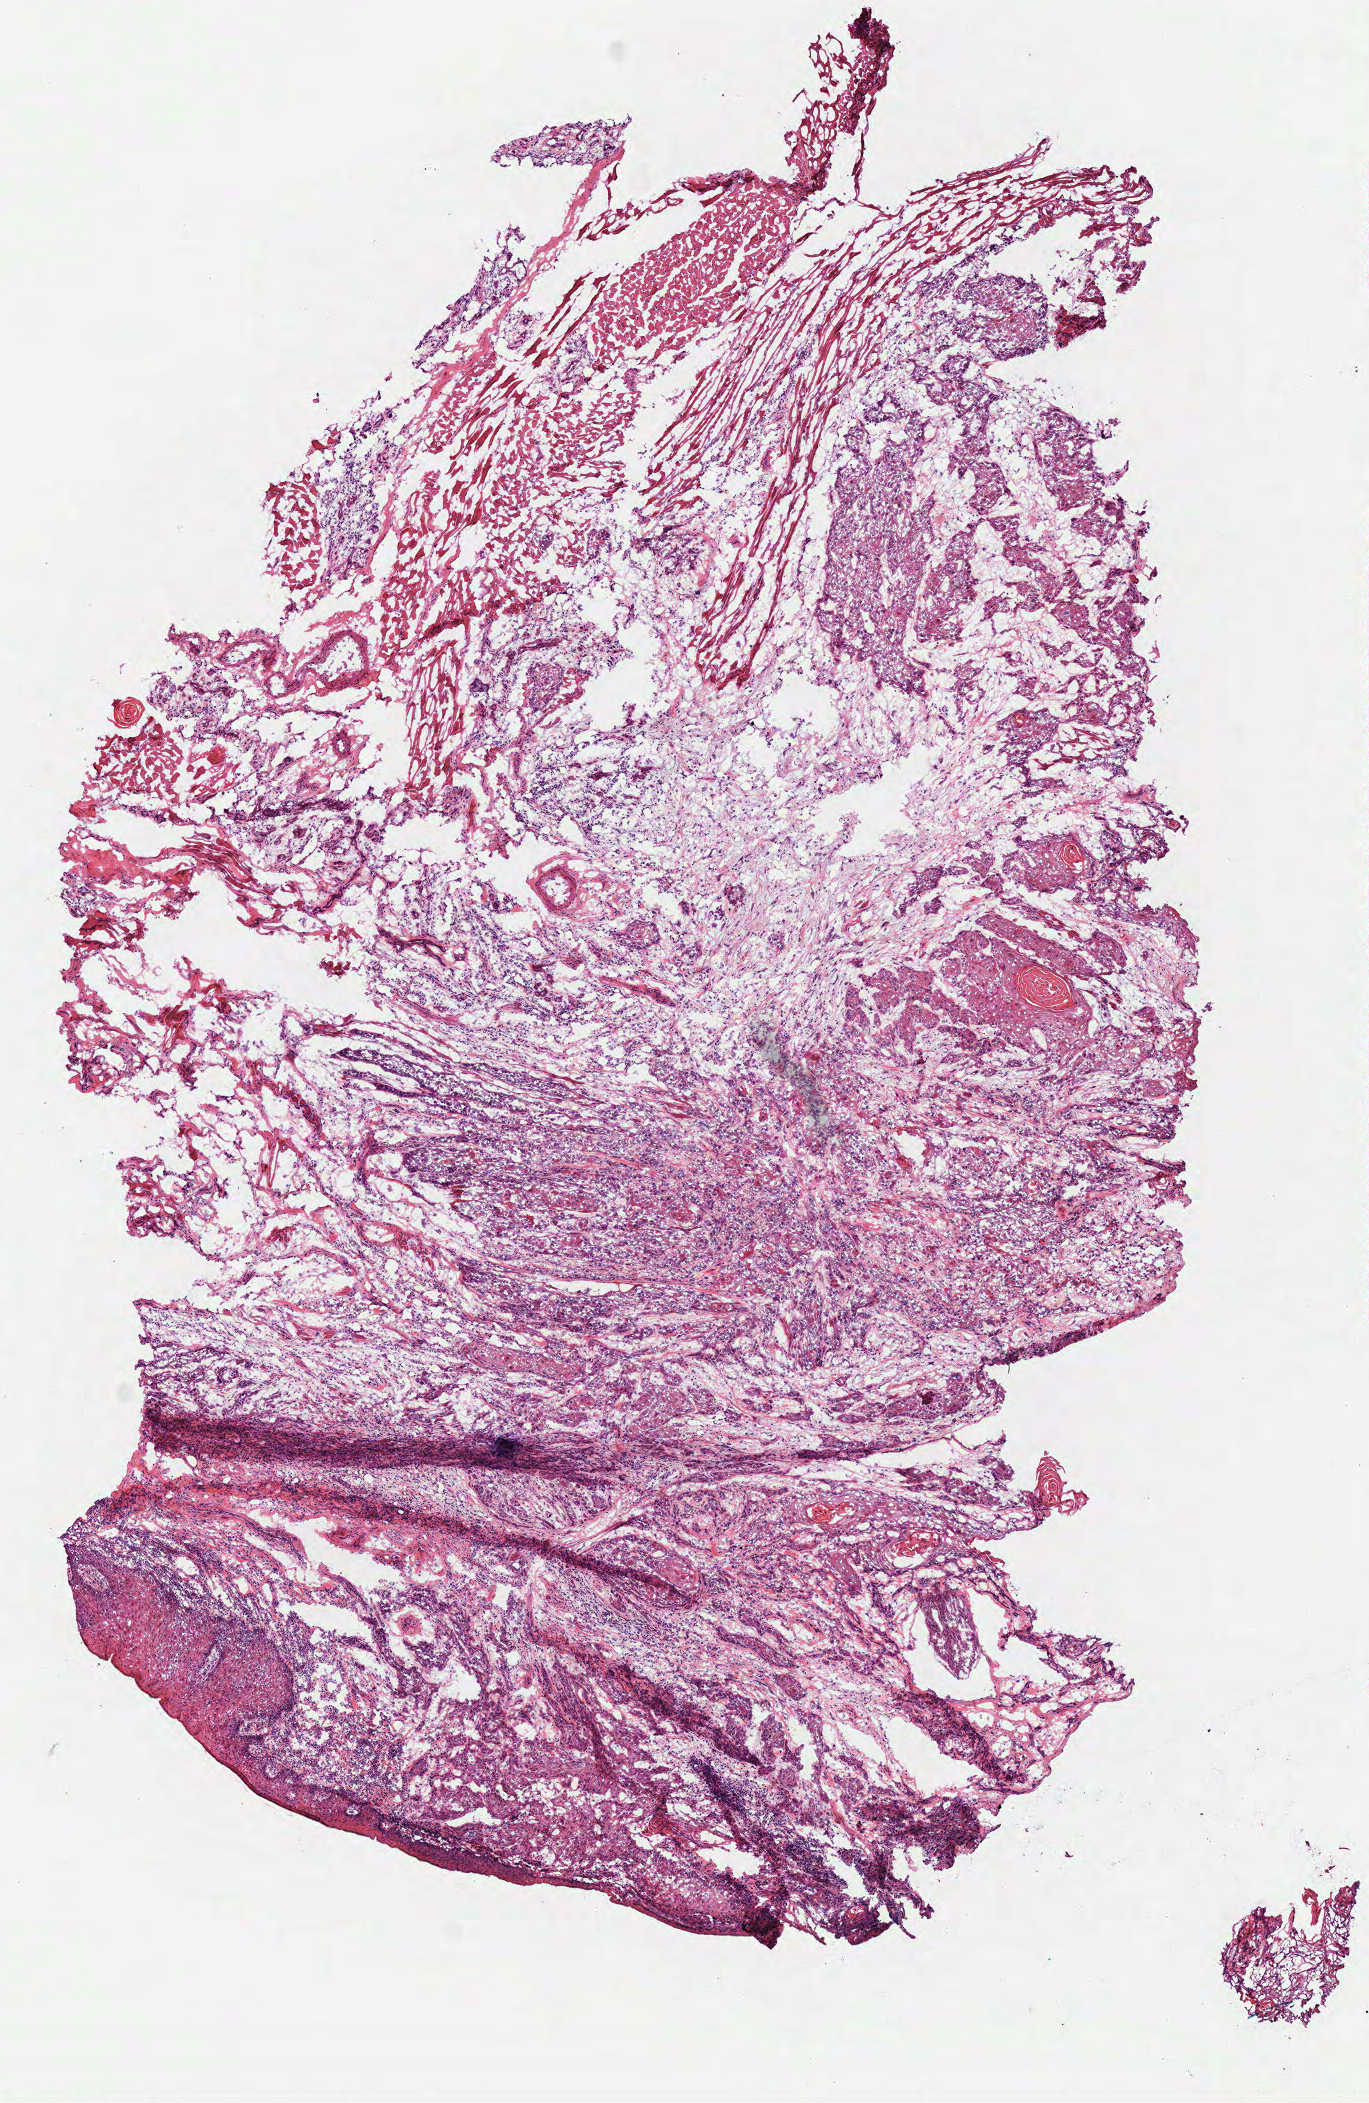
Hematoxylin and eosin (H&E) stained whole-slide image, shown as a low-resolution overview of the whole scanned area (about 5.4 x 8.3 mm, slide scanned at 40x); frozen section from the bottom of the tissue portion; sample: primary tumour, head and neck. Patient: female, age at initial diagnosis 61 years.
Histologic diagnosis: Squamous cell carcinoma, keratinizing, NOS (tongue, NOS).